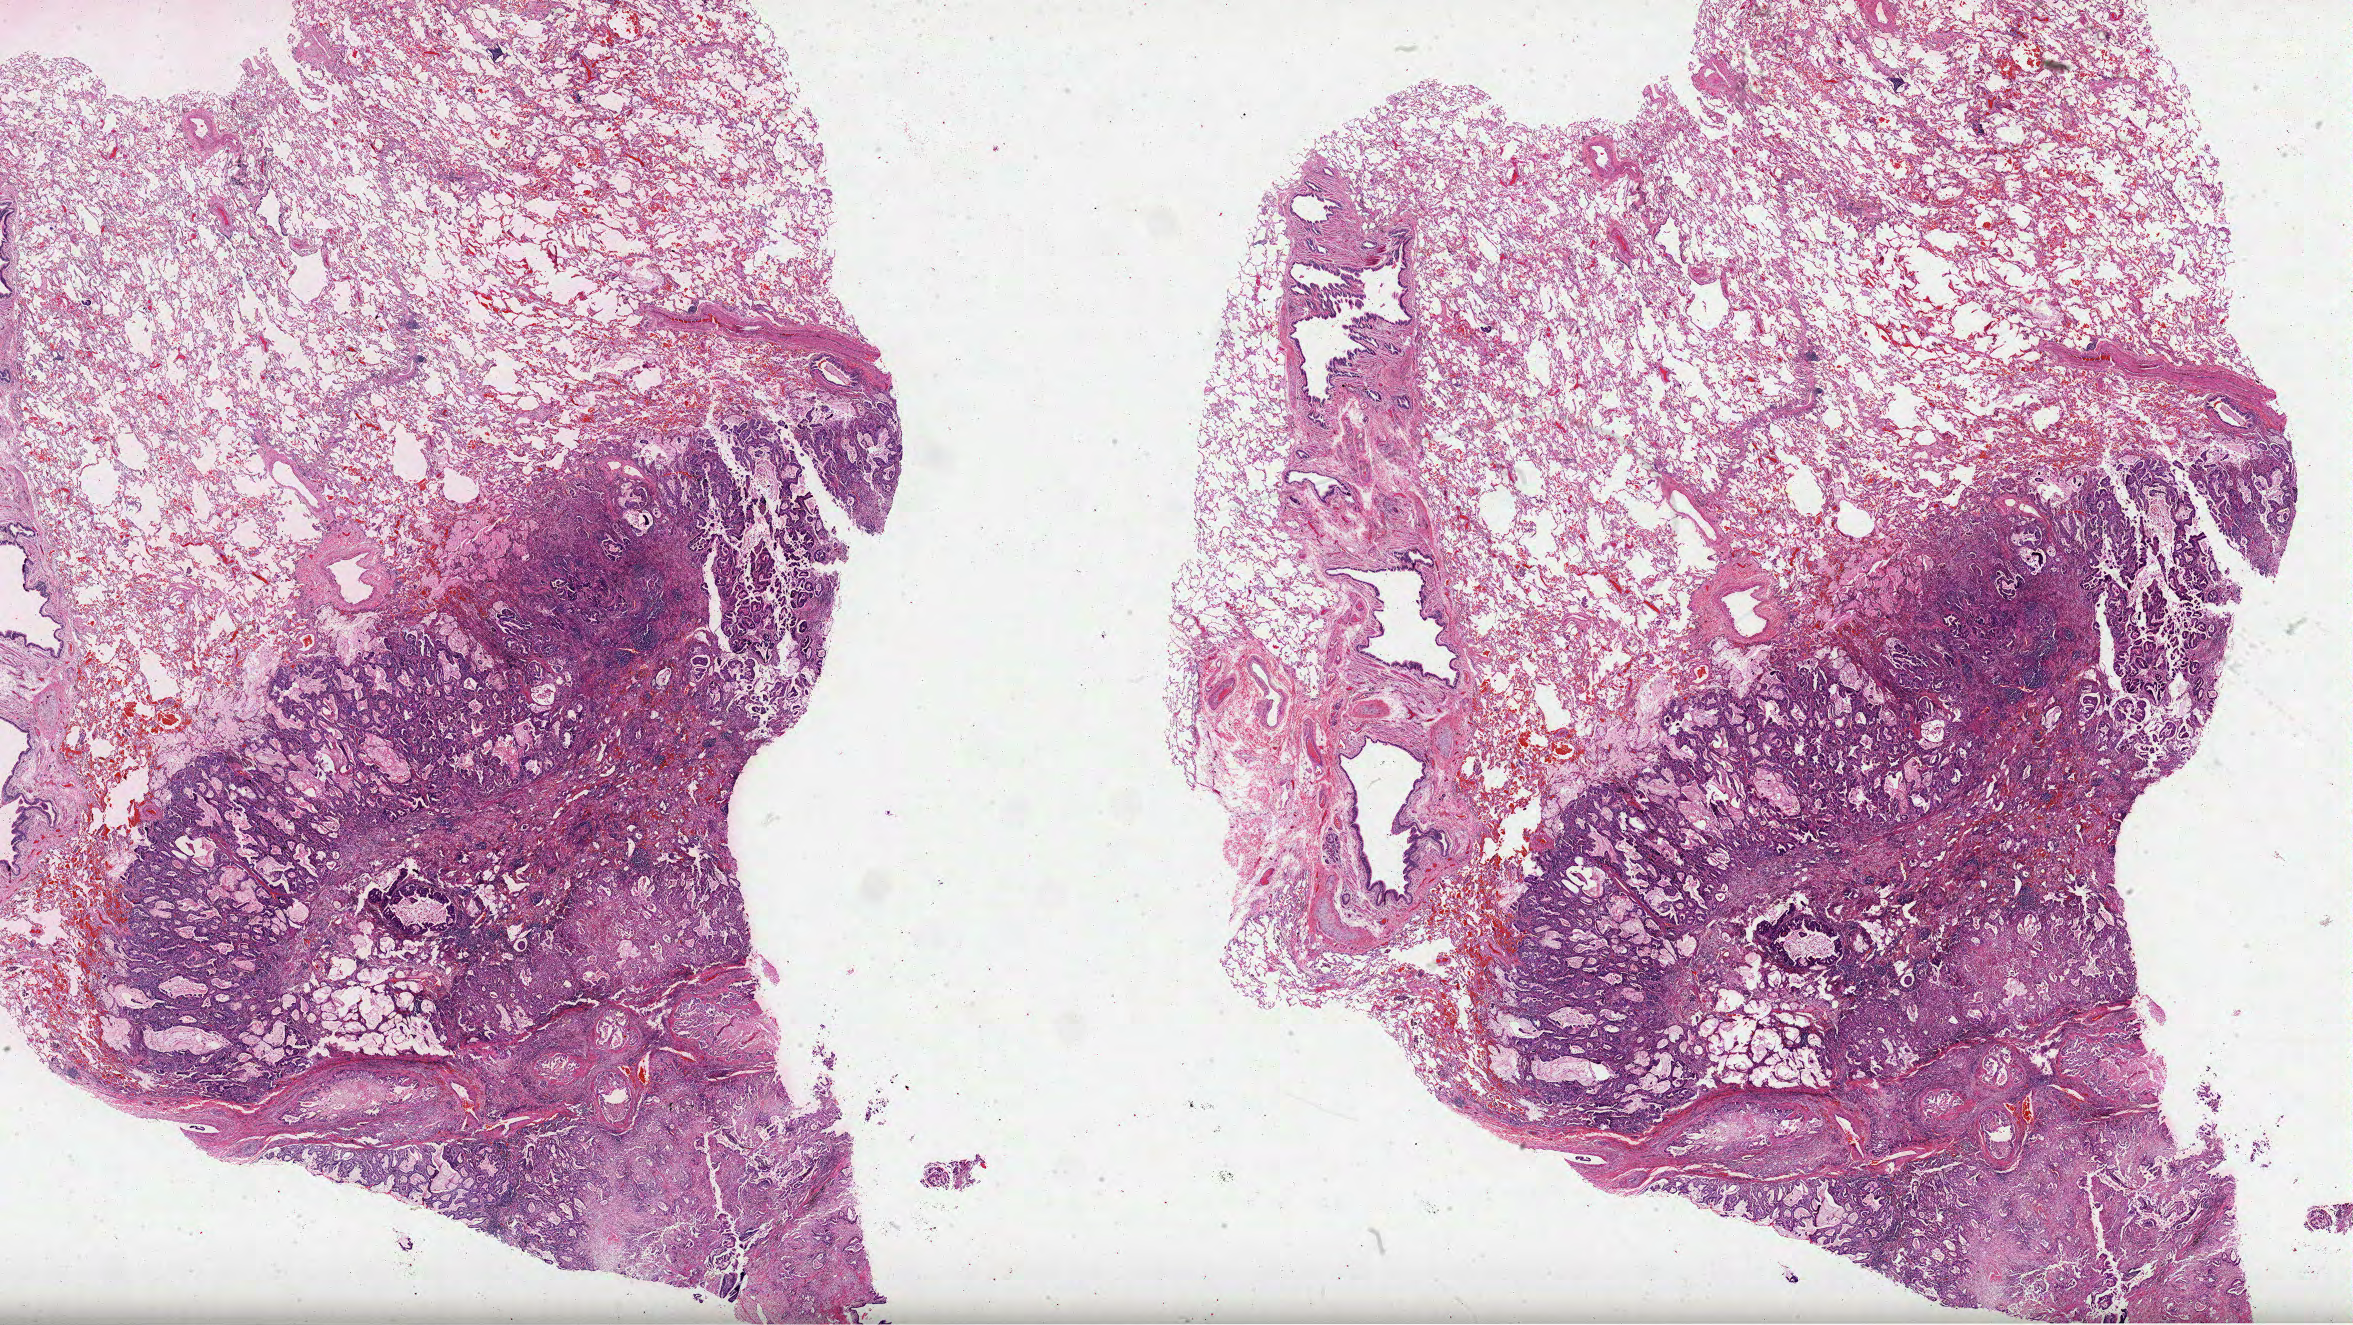
Digitized H&E tissue section (whole slide) — a low-resolution overview of the entire scanned area, about 38.0 x 21.4 mm (acquisition: 40x scan); formalin-fixed paraffin-embedded (FFPE) diagnostic section; primary tumour sample from the lung. Male, age 70 years at initial diagnosis.
Diagnosis: Mucinous adenocarcinoma (upper lobe, lung). AJCC pathologic stage: IIA (7th edition). Laterality: left.